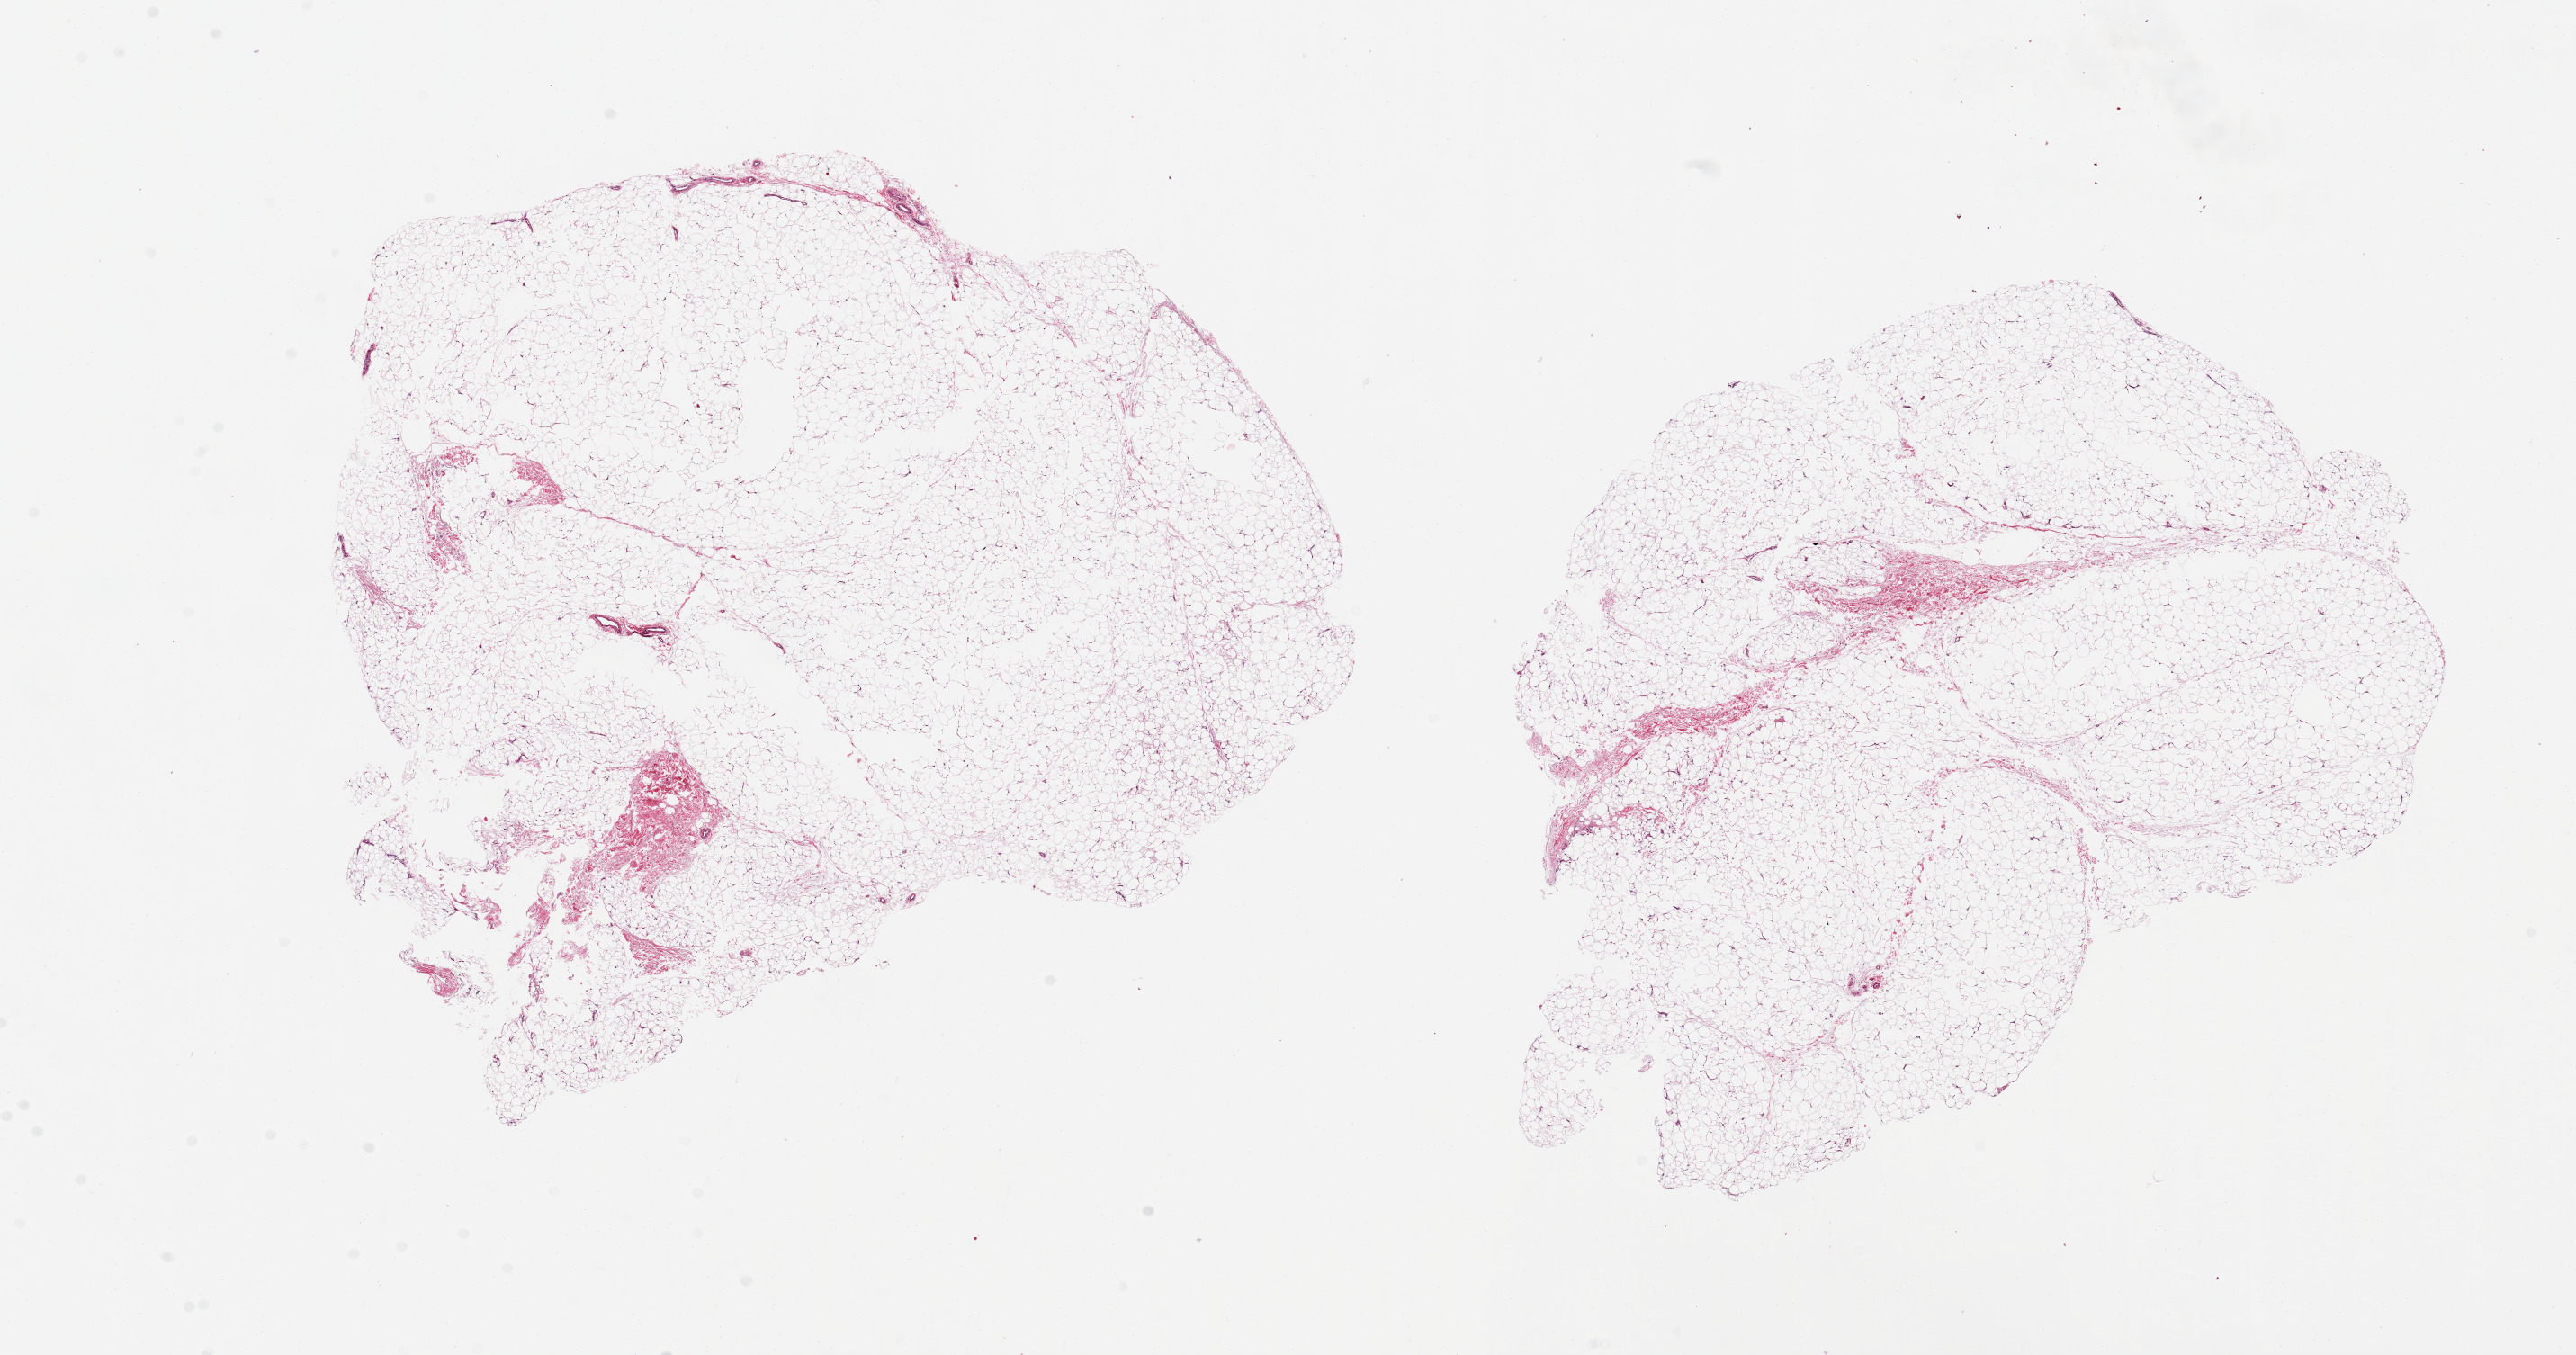
Digitized H&E-stained section, low-resolution overview of the scanned area, about 22.6 x 11.9 mm (from a 20x scan); PAXgene-fixed paraffin-embedded (PFPE) section; section of adipose tissue (target tissue); donor tissue sample.
- pathologist's review note for this sample: 2 pieces, 9x7 and 9x6 mm